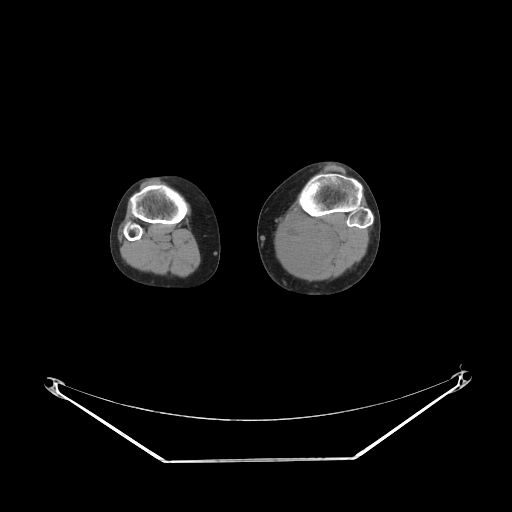
CT of an extremity soft-tissue mass (from a PET/CT study), one axial slice; position 157 of 223 along the scan axis; reconstruction kernel STANDARD; 140 kVp; soft-tissue window (W 400 / L 40 HU); 3.75 mm slice thickness; 512 × 512 image matrix, field of view 500 × 500 mm. Female patient. Case-level facts recorded for this patient, not image findings: histological type: extraskeletal high grade osteogenic sarcoma; grade: high; site of the primary tumour: left calf.
Annotated regions visible in this slice (expert contour drawn on MRI and transferred to this co-registered scan by the dataset authors):
- gross tumour volume (mass): bounding box (x1, y1, x2, y2) in pixels: (278, 224, 339, 271)